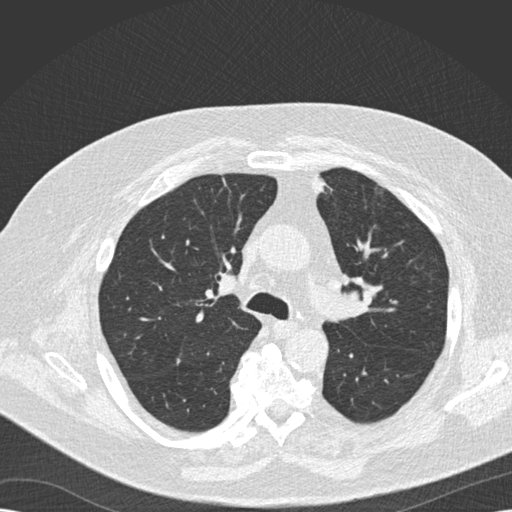
Low-dose screening chest CT, one axial slice; position 112 of 173 along the scan axis; reconstruction kernel B30f; lung window (W 1500 / L -600 HU); 2 mm slice thickness; 512 × 512 image matrix, field of view 370 × 370 mm.
Structures marked on this image (expert manual segmentation):
- lesion 1 (tumor, upper lobe of left lung): box from (x=314, y=176) to (x=326, y=194) px